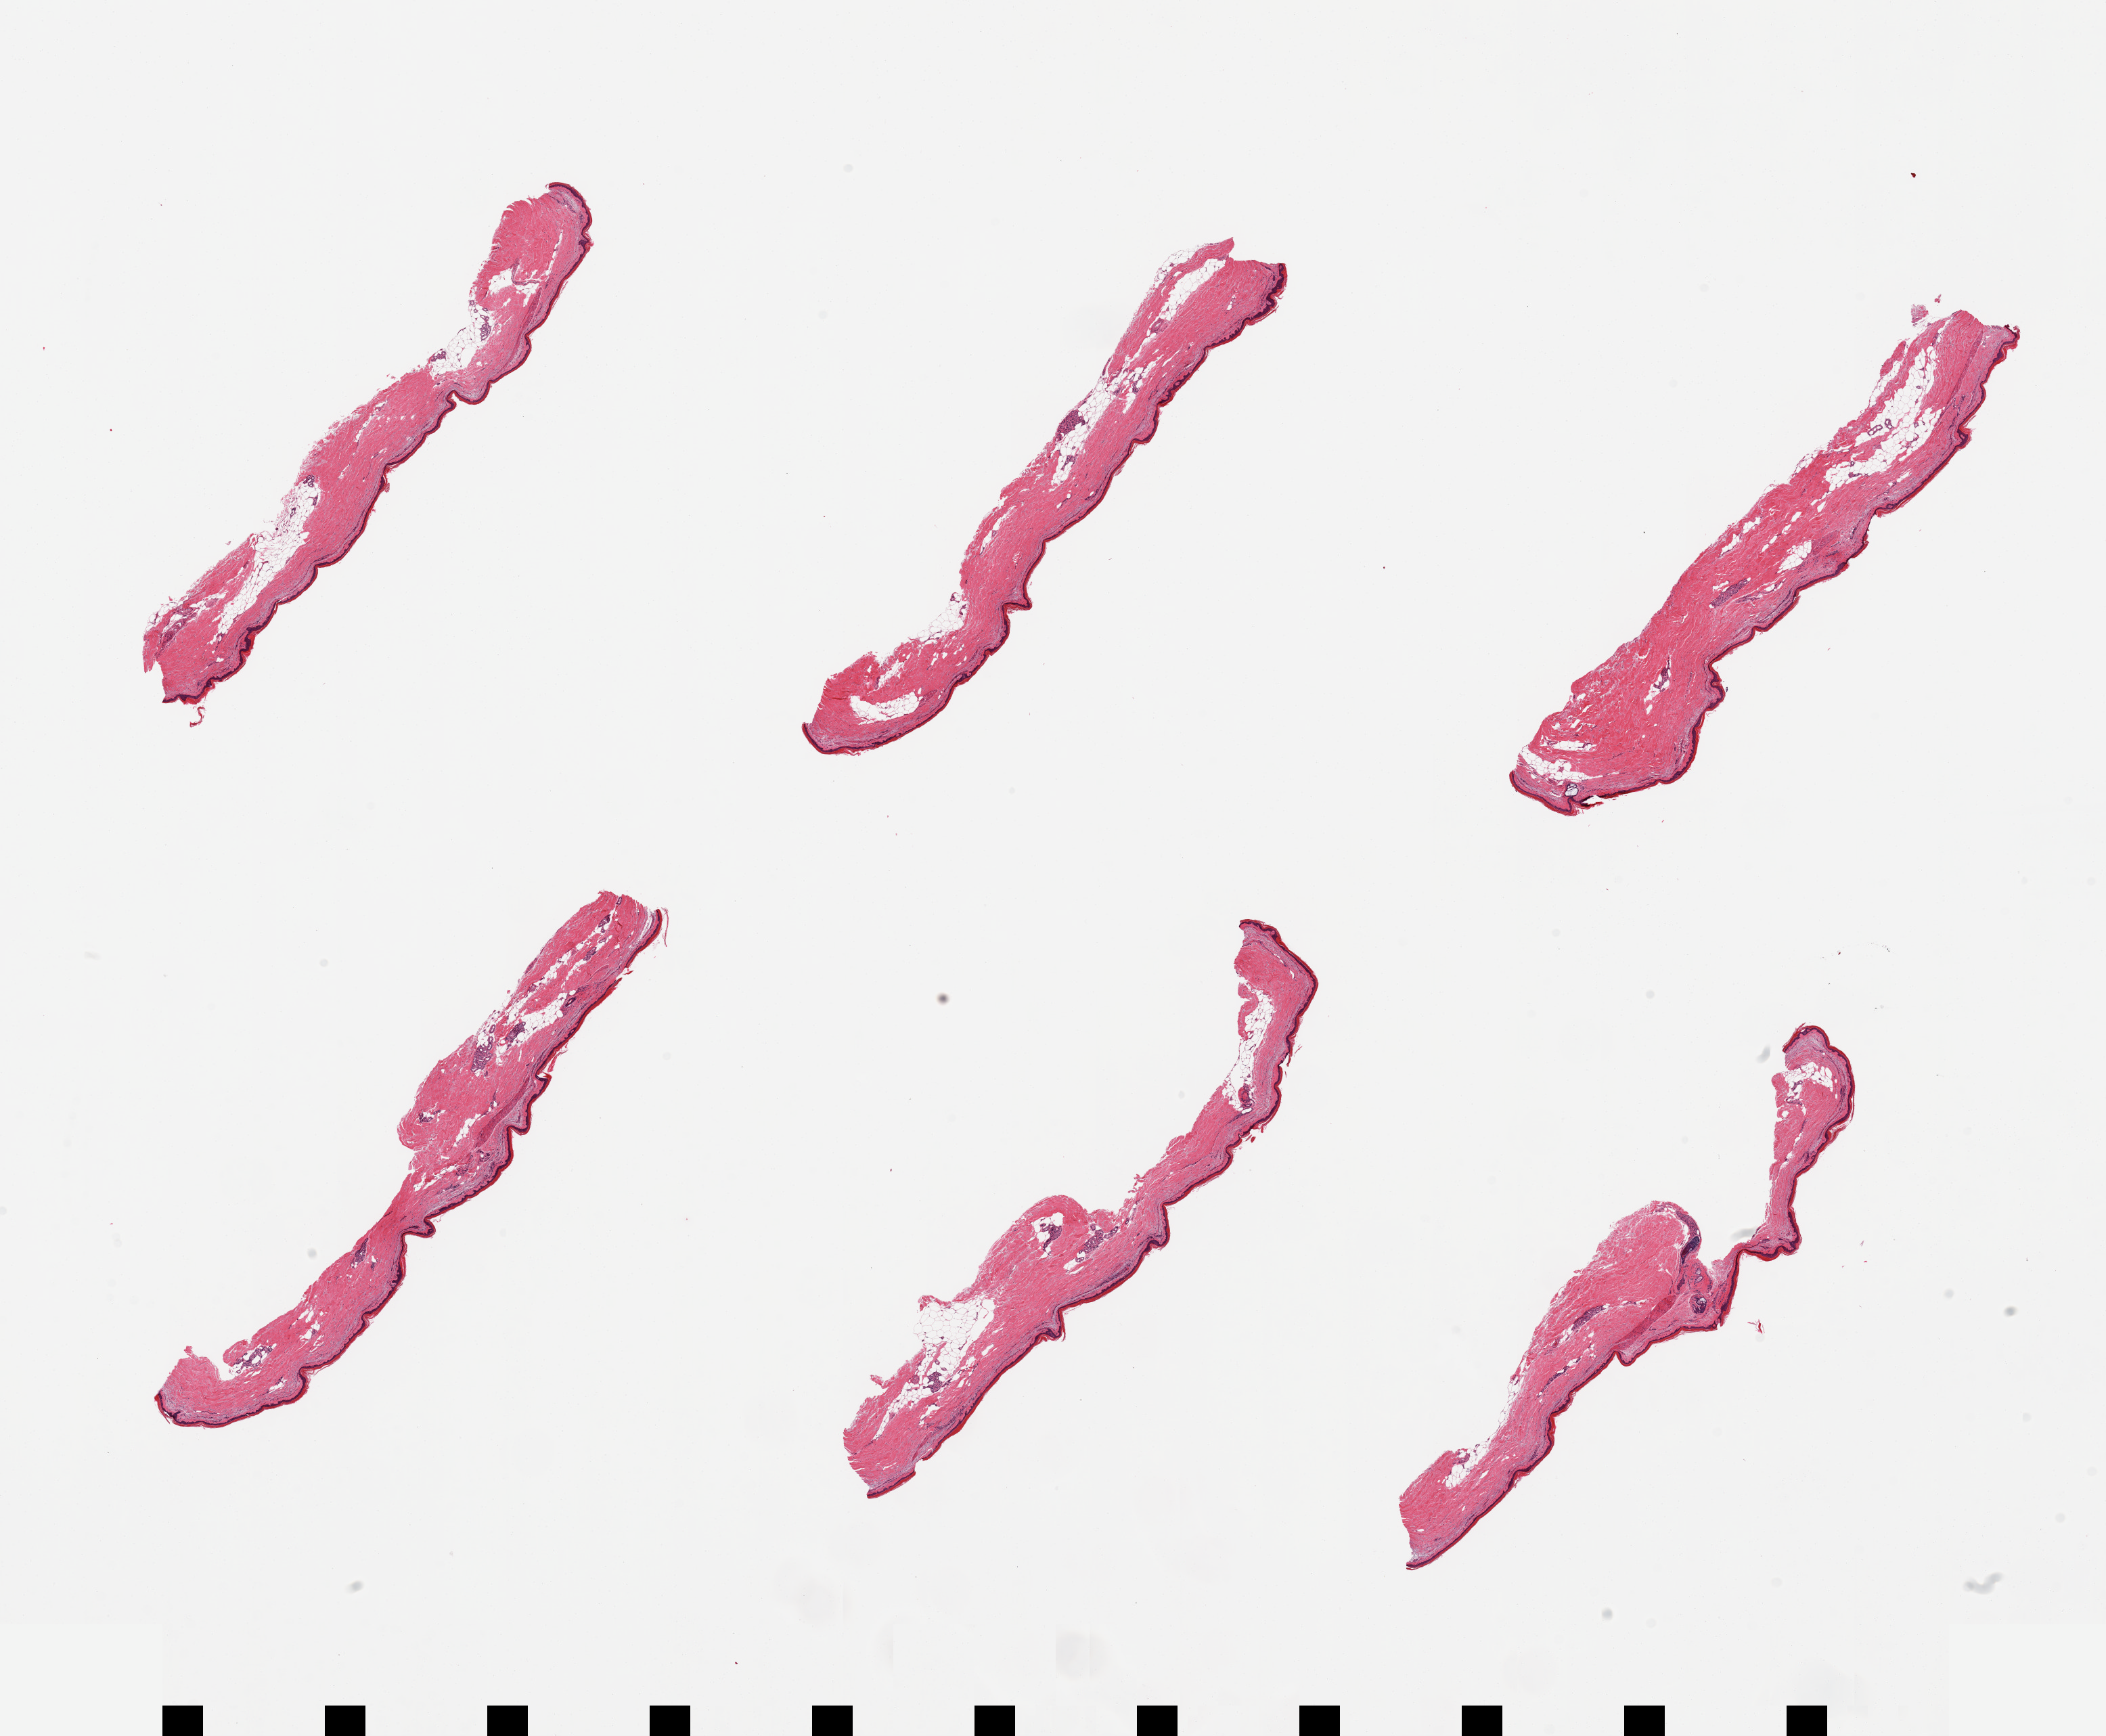
Digitized haematoxylin and eosin-stained section, low-resolution overview of the scanned area, about 24.6 x 20.3 mm (from a 20x scan); PAXgene-fixed paraffin-embedded (PFPE) section; section of skin of lower leg (target tissue); tissue donor sample. Male donor.
Reviewer comment on this tissue sample: 6 pieces; solar elastosis, attenuation of the epidermis:21.67um thick; up to 25% dermal fat.